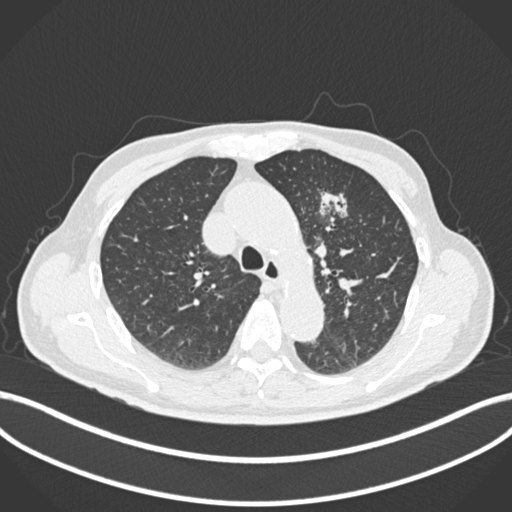
Chest CT, one axial slice; slice 177 of 261 in the series (ordered by position); reconstruction kernel B30f; lung window (W 1500 / L -600 HU); 1 mm slice thickness; 512 × 512 image matrix, field of view 400 × 400 mm. Male patient, age 74 years. From the clinical record (not read from this slice): clinical TNM (as recorded): T2b N0 M1c.
Structures marked on this image (bounding box drawn by a radiologist):
- lung tumour (recorded histology: adenocarcinoma): bounding box (x1, y1, x2, y2) in pixels: (311, 184, 356, 228)